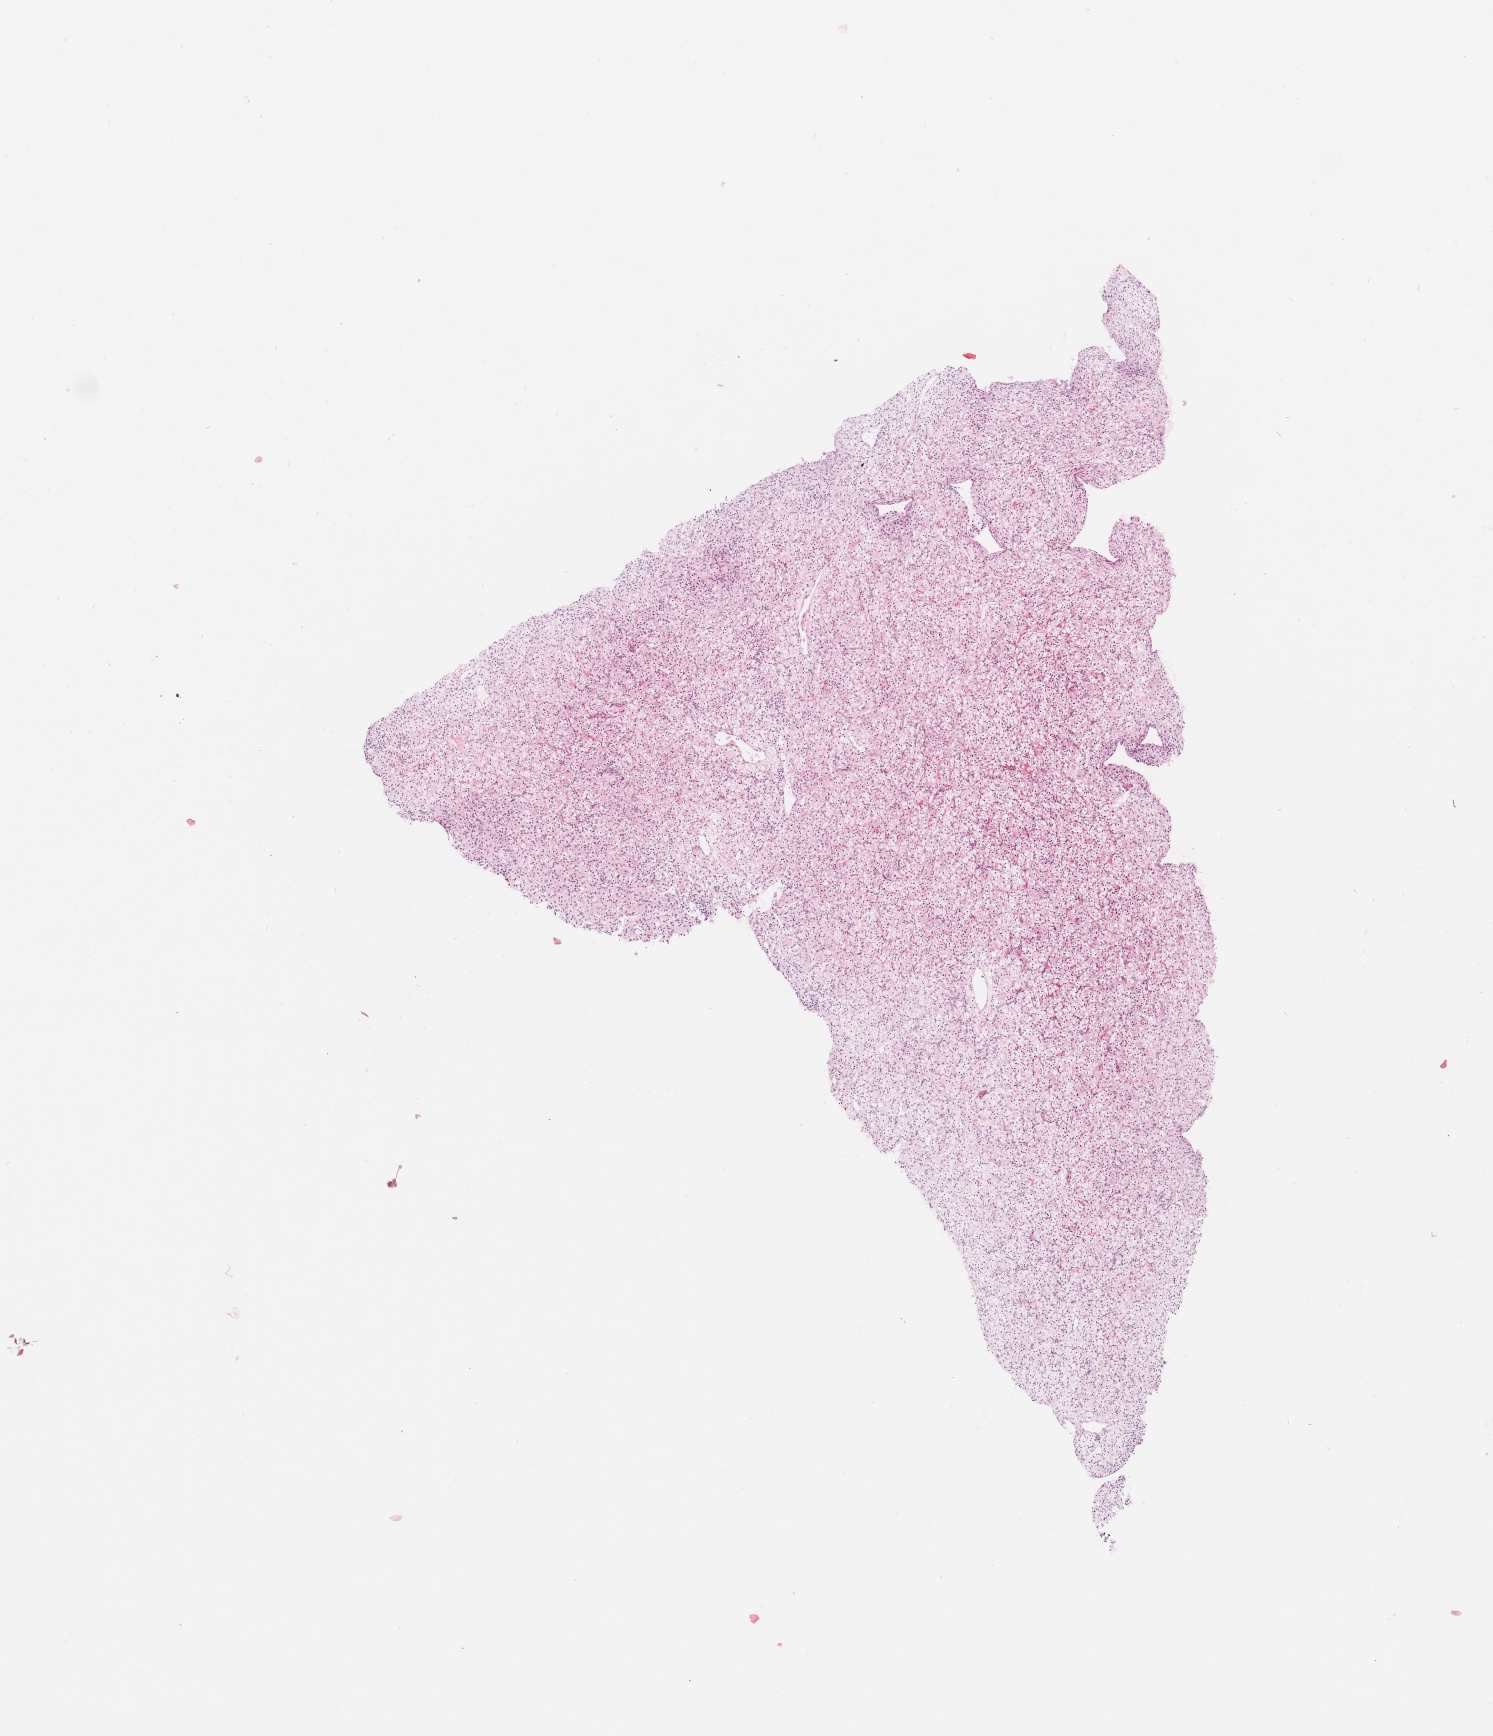
Digitized Hematoxylin and eosin (H&E) stained tissue section (whole slide) — low-resolution overview of the scanned area, about 5.9 x 6.9 mm (from a 20x scan); tumour tissue sample, sampled site: kidney. Patient: male, age 63 years. Histologic grade: G2 (moderately differentiated). Composition of this section per pathologist review: tumour nuclei 90%, necrosis 0%.
Primary tumour site (as recorded): lower pole. AJCC pathologic stage: I. Diagnosis: Renal cell carcinoma, NOS.